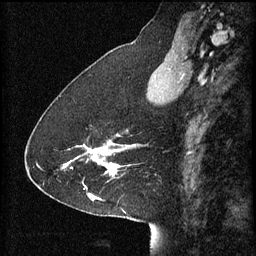
Breast MRI (dynamic contrast-enhanced), one sagittal slice. Position 23 of 60 along the scan axis. 3 images stored at this slice position (order not interpretable as contrast timing). 1.5 T. TE 4.2 ms, TR 8.2 ms. 2 mm slice thickness. 256 × 256 image matrix, field of view 200 × 200 mm. Patient: female, 41 years.
Structures marked on this image (semi-automatic segmentation, software-assisted and operator-edited):
- analysis volume of interest (the breast-tissue region the enhancement analysis was run in; not a lesion): box from (x=63, y=134) to (x=127, y=179) px
- tumour enhancement mask (voxels above the 70 % enhancement threshold inside the analysis volume of interest): (x=63, y=134)–(x=127, y=177)